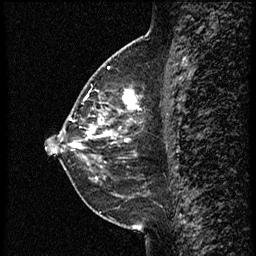
Breast MRI (dynamic contrast-enhanced), one sagittal slice; slice 26 of 60 in the series (ordered by position); dynamic contrast-enhanced study with each time point stored as its own series, time point 2 of 3 at this slice position (early post-contrast, ordered by acquisition time); 1.5 T; TE 4.2 ms, TR 18.9 ms; 2 mm slice thickness; 256 × 256 image matrix, field of view 200 × 200 mm. Female patient. Case-level facts recorded for this patient, not image findings: setting: breast cancer imaged before/during neoadjuvant chemotherapy; receptor status: HER2-positive.
Outlined on this slice (semi-automatically segmented with operator editing):
- analysis volume of interest (the breast-tissue region the enhancement analysis was run in; not a lesion): bounding box (x1, y1, x2, y2) in pixels: (77, 85, 147, 147)
- tumour enhancement mask (voxels above the 100 % enhancement threshold inside the analysis volume of interest): (77, 89, 138, 147)